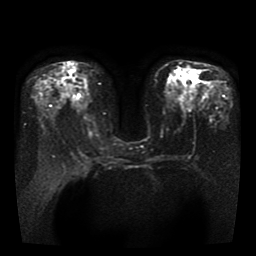
Breast MRI, one axial slice; slice 19 of 41 in the series (ordered by position); diffusion-weighted series; image 2 of 4 stored at this slice position (different b-values; order by instance number); 1.5 T; 5 mm slice thickness; 256 × 256 image matrix. Female patient.
Annotated regions visible in this slice (manually delineated by an expert):
- tumour on diffusion-weighted imaging: bounding box (x1, y1, x2, y2) in pixels: (170, 92, 177, 98)